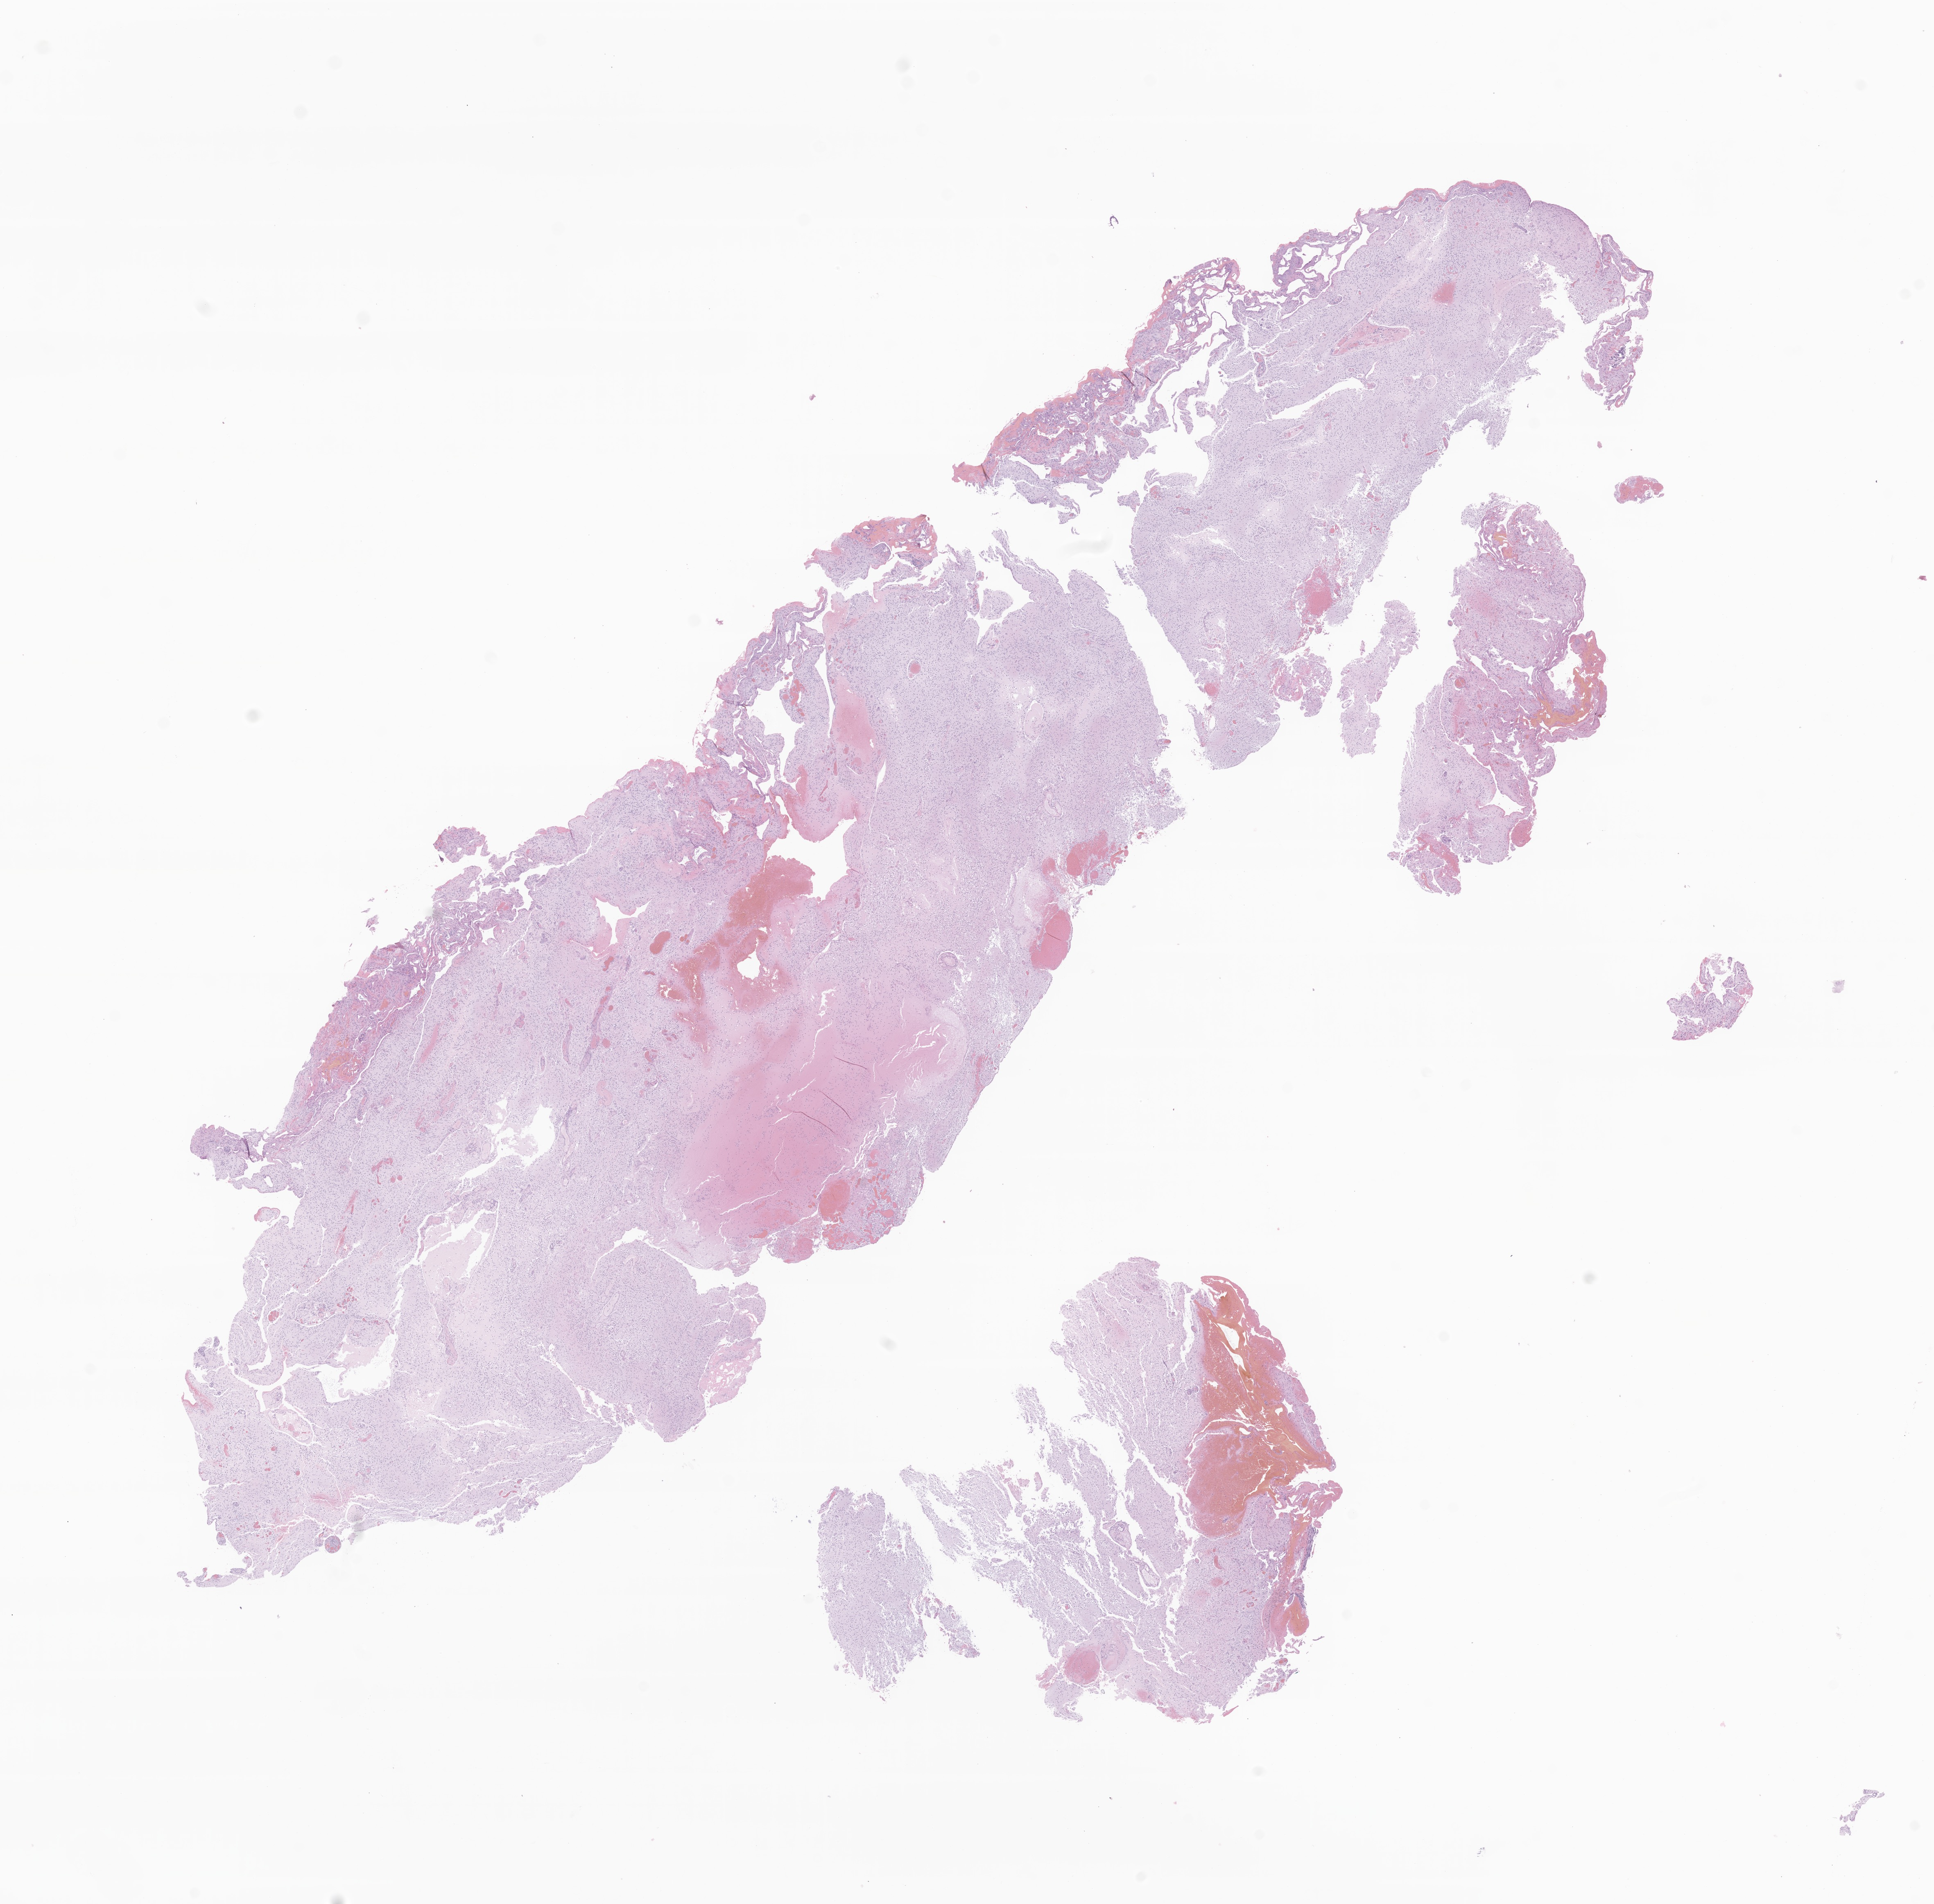
Hematoxylin and eosin (H&E) whole-slide image of tumor tissue from the brain — low-resolution overview of the scanned area, about 19.9 x 19.6 mm. Formalin-fixed paraffin-embedded section. Patient: male, age 76 months (6 years 4 months).
Recorded diagnosis: Pilocytic astrocytoma.